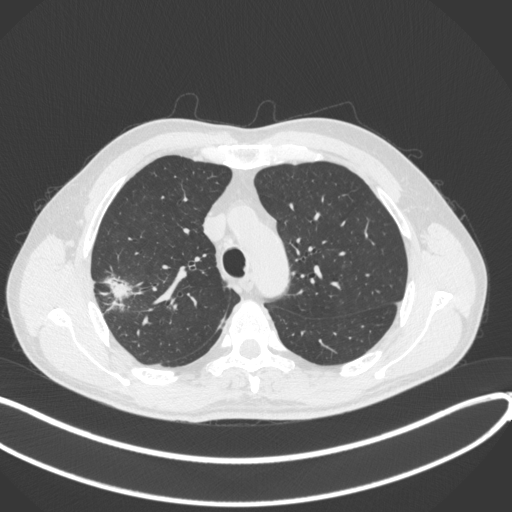
Chest CT, one axial slice. Position 311 of 381 along the scan axis. Reconstruction kernel B31f. 120 kVp. Lung window (W 1500 / L -600 HU). 1 mm slice thickness. 512 × 512 image matrix, field of view 400 × 400 mm. Male patient, age 62 years. From the clinical record (not read from this slice): clinical TNM (as recorded): T1c N0 M0; histopathological grade: G2-3.
Annotated regions visible in this slice (bounding box drawn by a radiologist):
- lung tumour (recorded histology: adenocarcinoma): bounding box <100,268,136,313> (left, top, right, bottom; pixels)